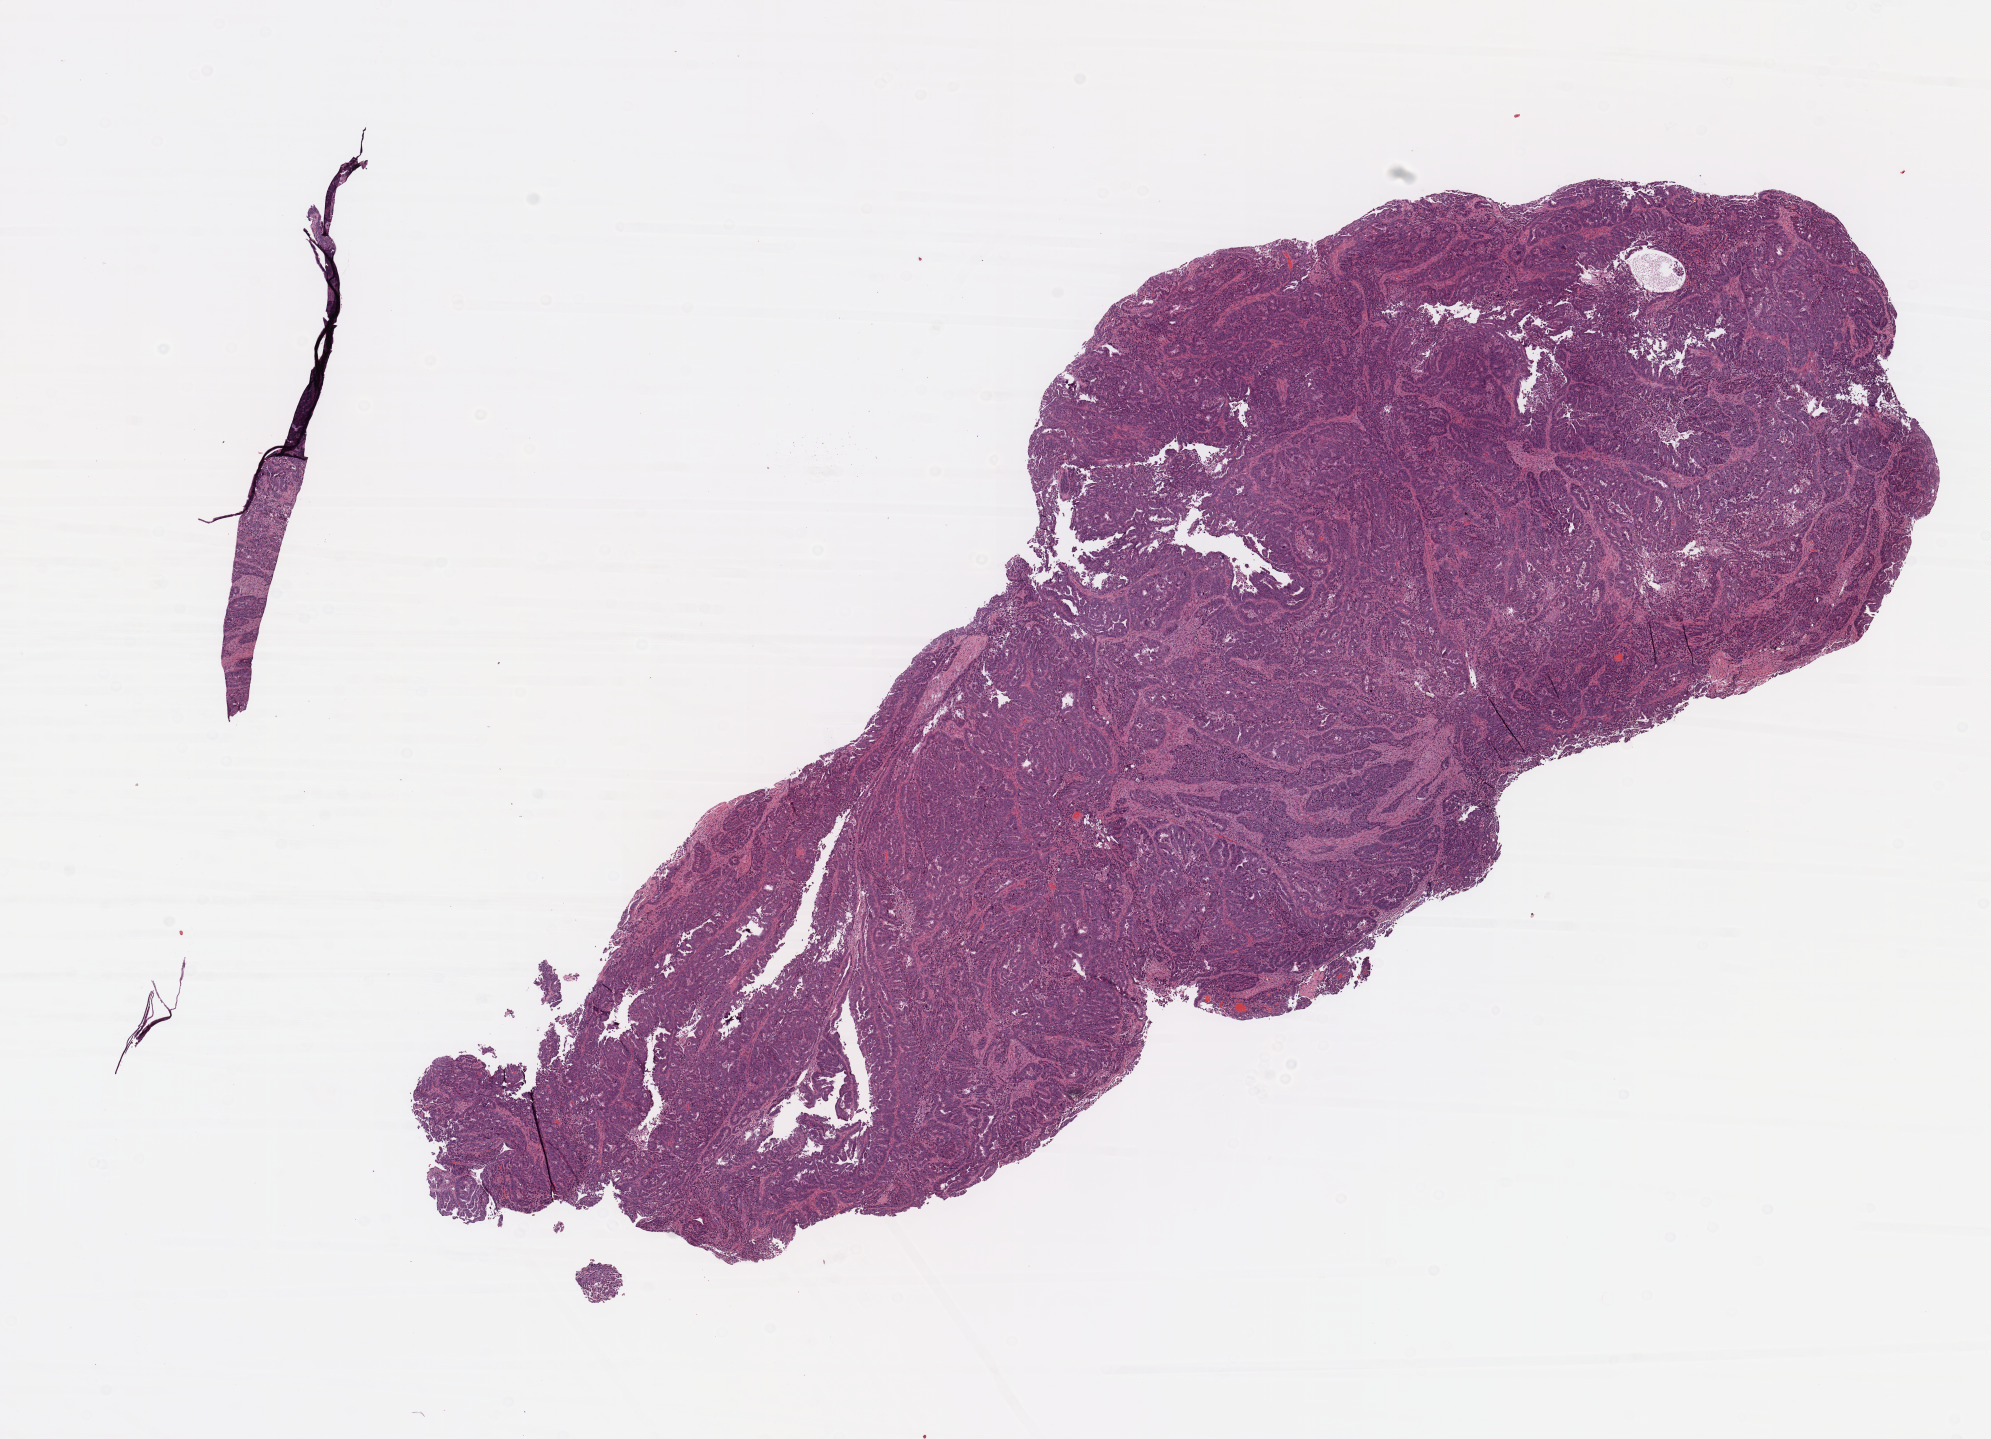
Digitized H&E tissue section (whole slide), low-resolution overview of the scanned area, about 15.8 x 11.4 mm (slide scanned at 20x), tumour tissue sample, sampled site: uterus. 67-year-old female patient. Histologic grade: G3 (poorly differentiated). Composition of this section per pathologist review: tumour nuclei 90%, necrosis 2%.
* AJCC pathologic stage: IB
* histologic diagnosis: Endometrioid adenocarcinoma, NOS